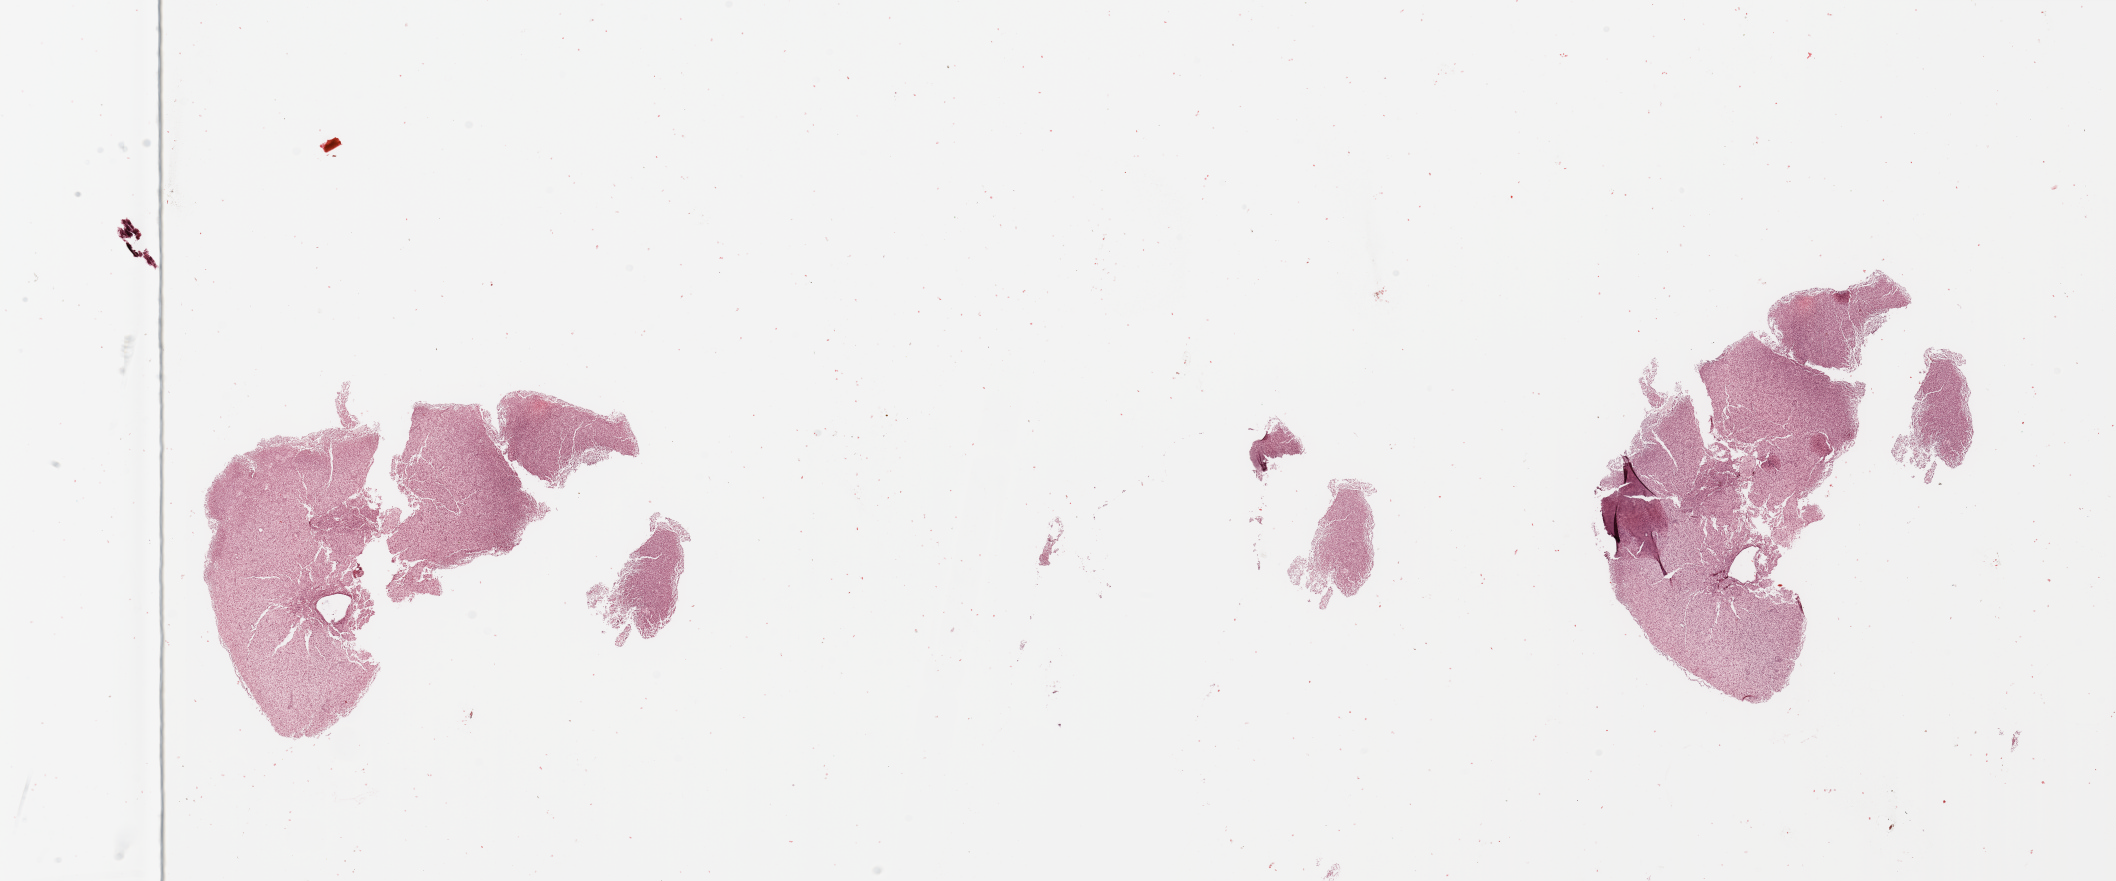
Digitized Hematoxylin and eosin (H&E) stained tissue section (whole slide) — shown as a low-resolution overview of the whole scanned area (about 33.5 x 13.9 mm, from a 20x scan); tumour tissue sample, sampled site: brain. 69-year-old female patient. Composition of this section per pathologist review: tumour nuclei 90%, necrosis 2%.
• diagnosis: Glioblastoma
• primary tumour site (as recorded): temporal lobe